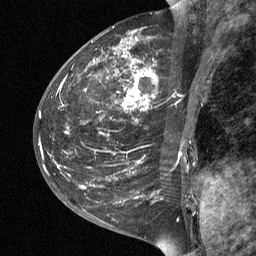
Breast MRI (dynamic contrast-enhanced), one sagittal slice; slice 22 of 64 in the series (ordered by position); dynamic contrast-enhanced study with each time point stored as its own series, time point 2 of 3 at this slice position (early post-contrast, ordered by acquisition time); 1.5 T; TE 4.8 ms, TR 27 ms; 256 × 256 image matrix. Patient: female, 42 years. Case-level facts recorded for this patient, not image findings: setting: breast cancer imaged before/during neoadjuvant chemotherapy; receptor status: triple-negative.
Structures marked on this image (semi-automatic segmentation, software-assisted and operator-edited):
- analysis volume of interest (the breast-tissue region the enhancement analysis was run in; not a lesion): bounding box <43,29,203,190> (left, top, right, bottom; pixels)
- tumour enhancement mask (voxels above the 90 % enhancement threshold inside the analysis volume of interest): <81,53,153,188>